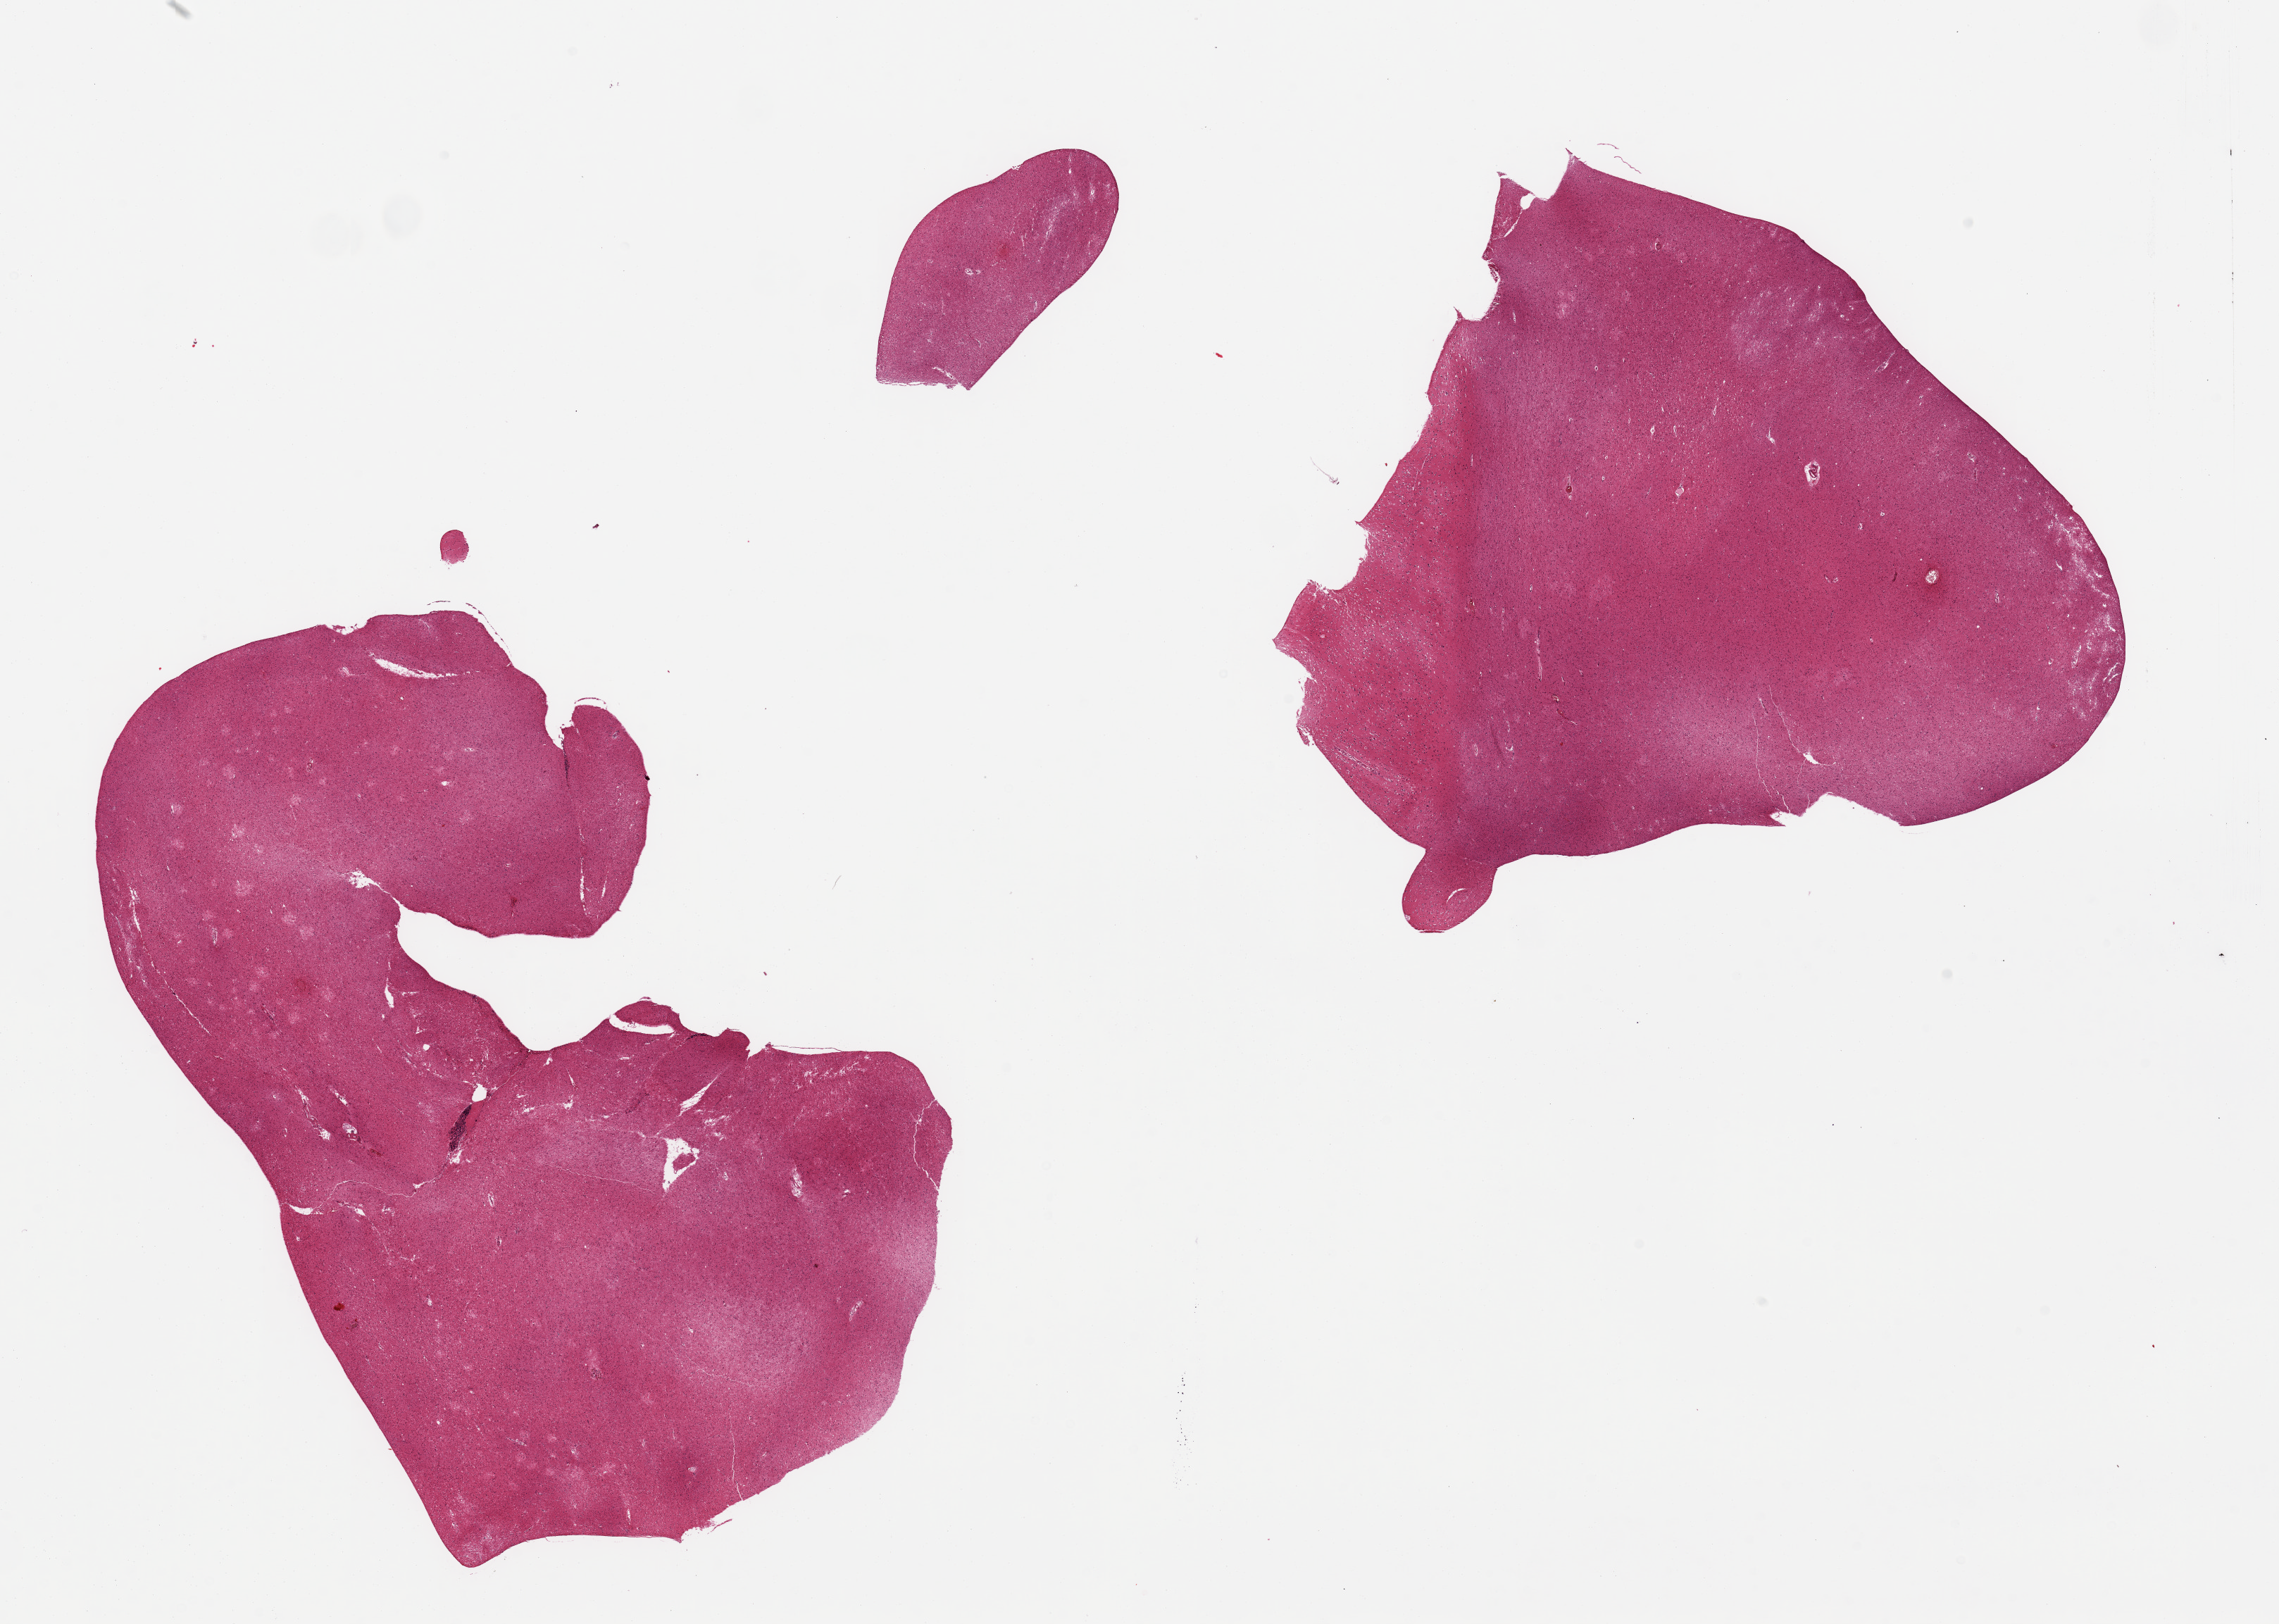
Haematoxylin and eosin whole-slide image, shown as a low-resolution overview of the whole scanned area (about 25.6 x 18.2 mm), PAXgene-fixed paraffin-embedded (PFPE) section, sampled site (target tissue): cerebral cortex, donor tissue sample. Donor: male.
Reviewer comment on this tissue sample: 2 pieces, no abnormalities.